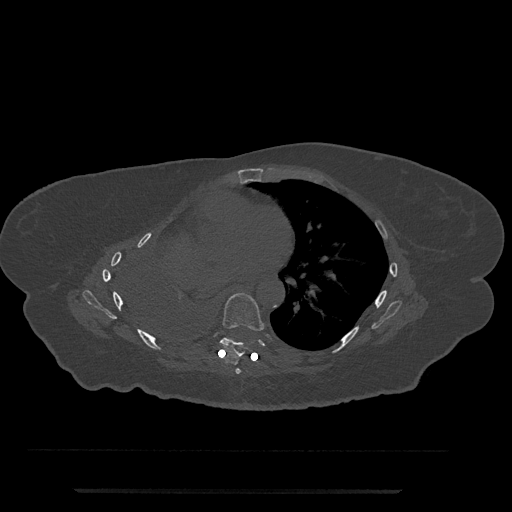
CT including the spine, one axial slice. Position 437 of 797 along the scan axis. 120 kVp. Bone window (W 1800 / L 400 HU). 0.5 mm slice thickness. 512 × 512 image matrix, field of view 440 × 440 mm. Patient: female, 51 years. Case-level facts recorded for this patient, not image findings: primary cancer: neuro; vertebrae with lytic lesions (as recorded): T8.
Annotated regions visible in this slice (semi-automatic segmentation, software-assisted and operator-edited):
- T6 vertebra: bounding box (x1, y1, x2, y2) in pixels: (235, 368, 241, 374)
- T7 vertebra: (220, 293, 265, 365)
- T8 vertebra: (225, 337, 229, 339)